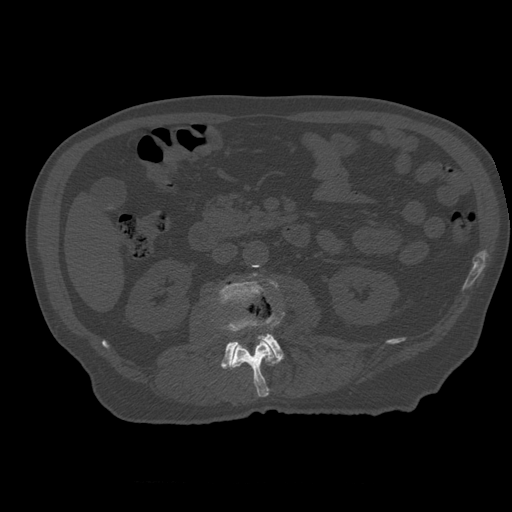
CT including the spine, one axial slice. 120 kVp. Bone window (W 1800 / L 400 HU). 512 × 512 image matrix, field of view 407 × 407 mm. Patient age 73 years. Case-level facts recorded for this patient, not image findings: primary cancer: prostate.
Outlined on this slice (semi-automatic segmentation, software-assisted and operator-edited):
- L2 vertebra: bounding box (x1, y1, x2, y2) in pixels: (230, 312, 285, 398)
- L3 vertebra: (219, 274, 285, 369)